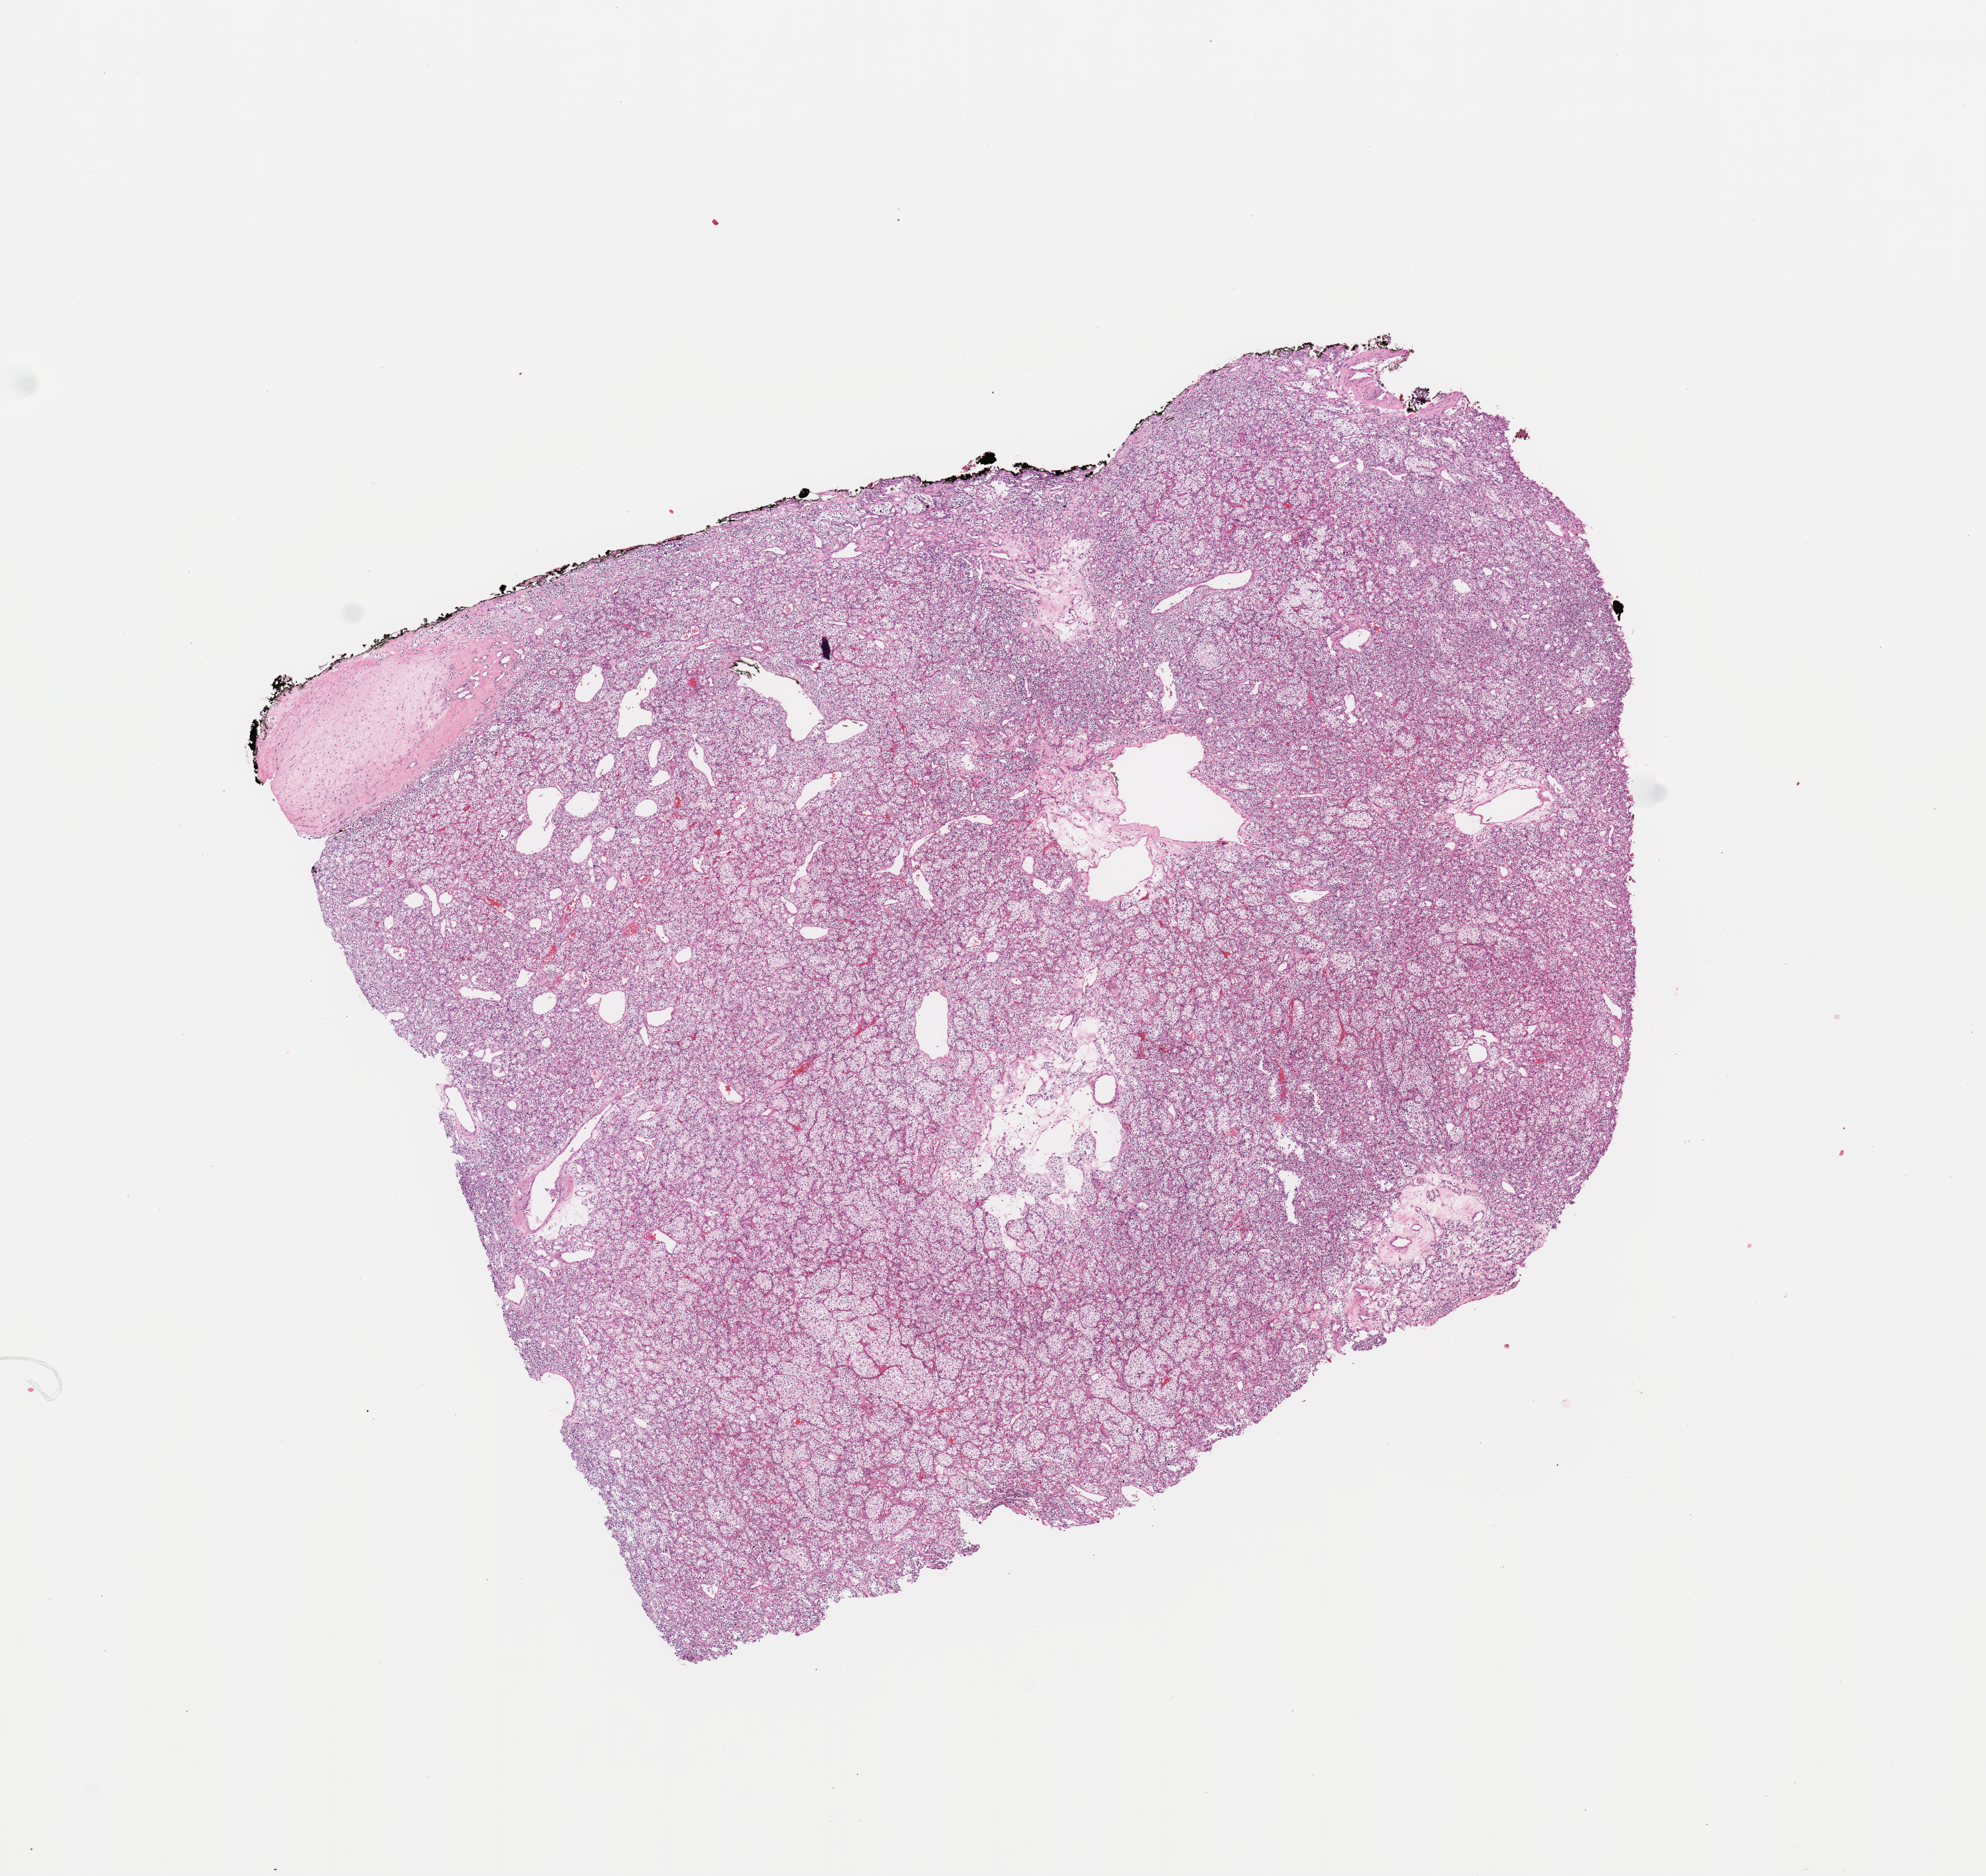
Digitized Hematoxylin and eosin (H&E) stained tissue section (whole slide) — low-resolution overview of the scanned area, about 11.8 x 11.2 mm (from a 20x scan). Tumour tissue sample, sampled site: kidney. Patient: female, age 51 years. Histologic grade: G3 (poorly differentiated). Composition of this section per pathologist review: tumour nuclei 85%, necrosis 0%.
Diagnosis: Renal cell carcinoma, NOS. AJCC pathologic stage: II.